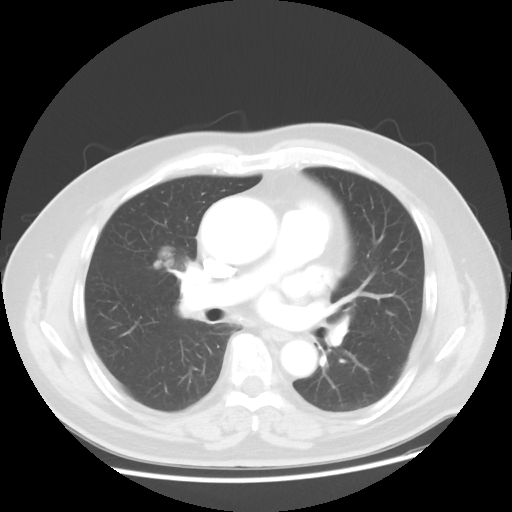
Chest CT, one axial slice; position 24 of 48 along the scan axis; lung window (W 1500 / L -600 HU); 5 mm slice thickness; 512 × 512 image matrix. Patient: male, 60 years. From the clinical record (not read from this slice): clinical TNM (as recorded): T2 N3 M0.
Annotated regions visible in this slice (bounding box drawn by a radiologist):
- lung tumour (recorded histology: adenocarcinoma): bounding box [x1, y1, x2, y2] px = [146, 242, 200, 290]